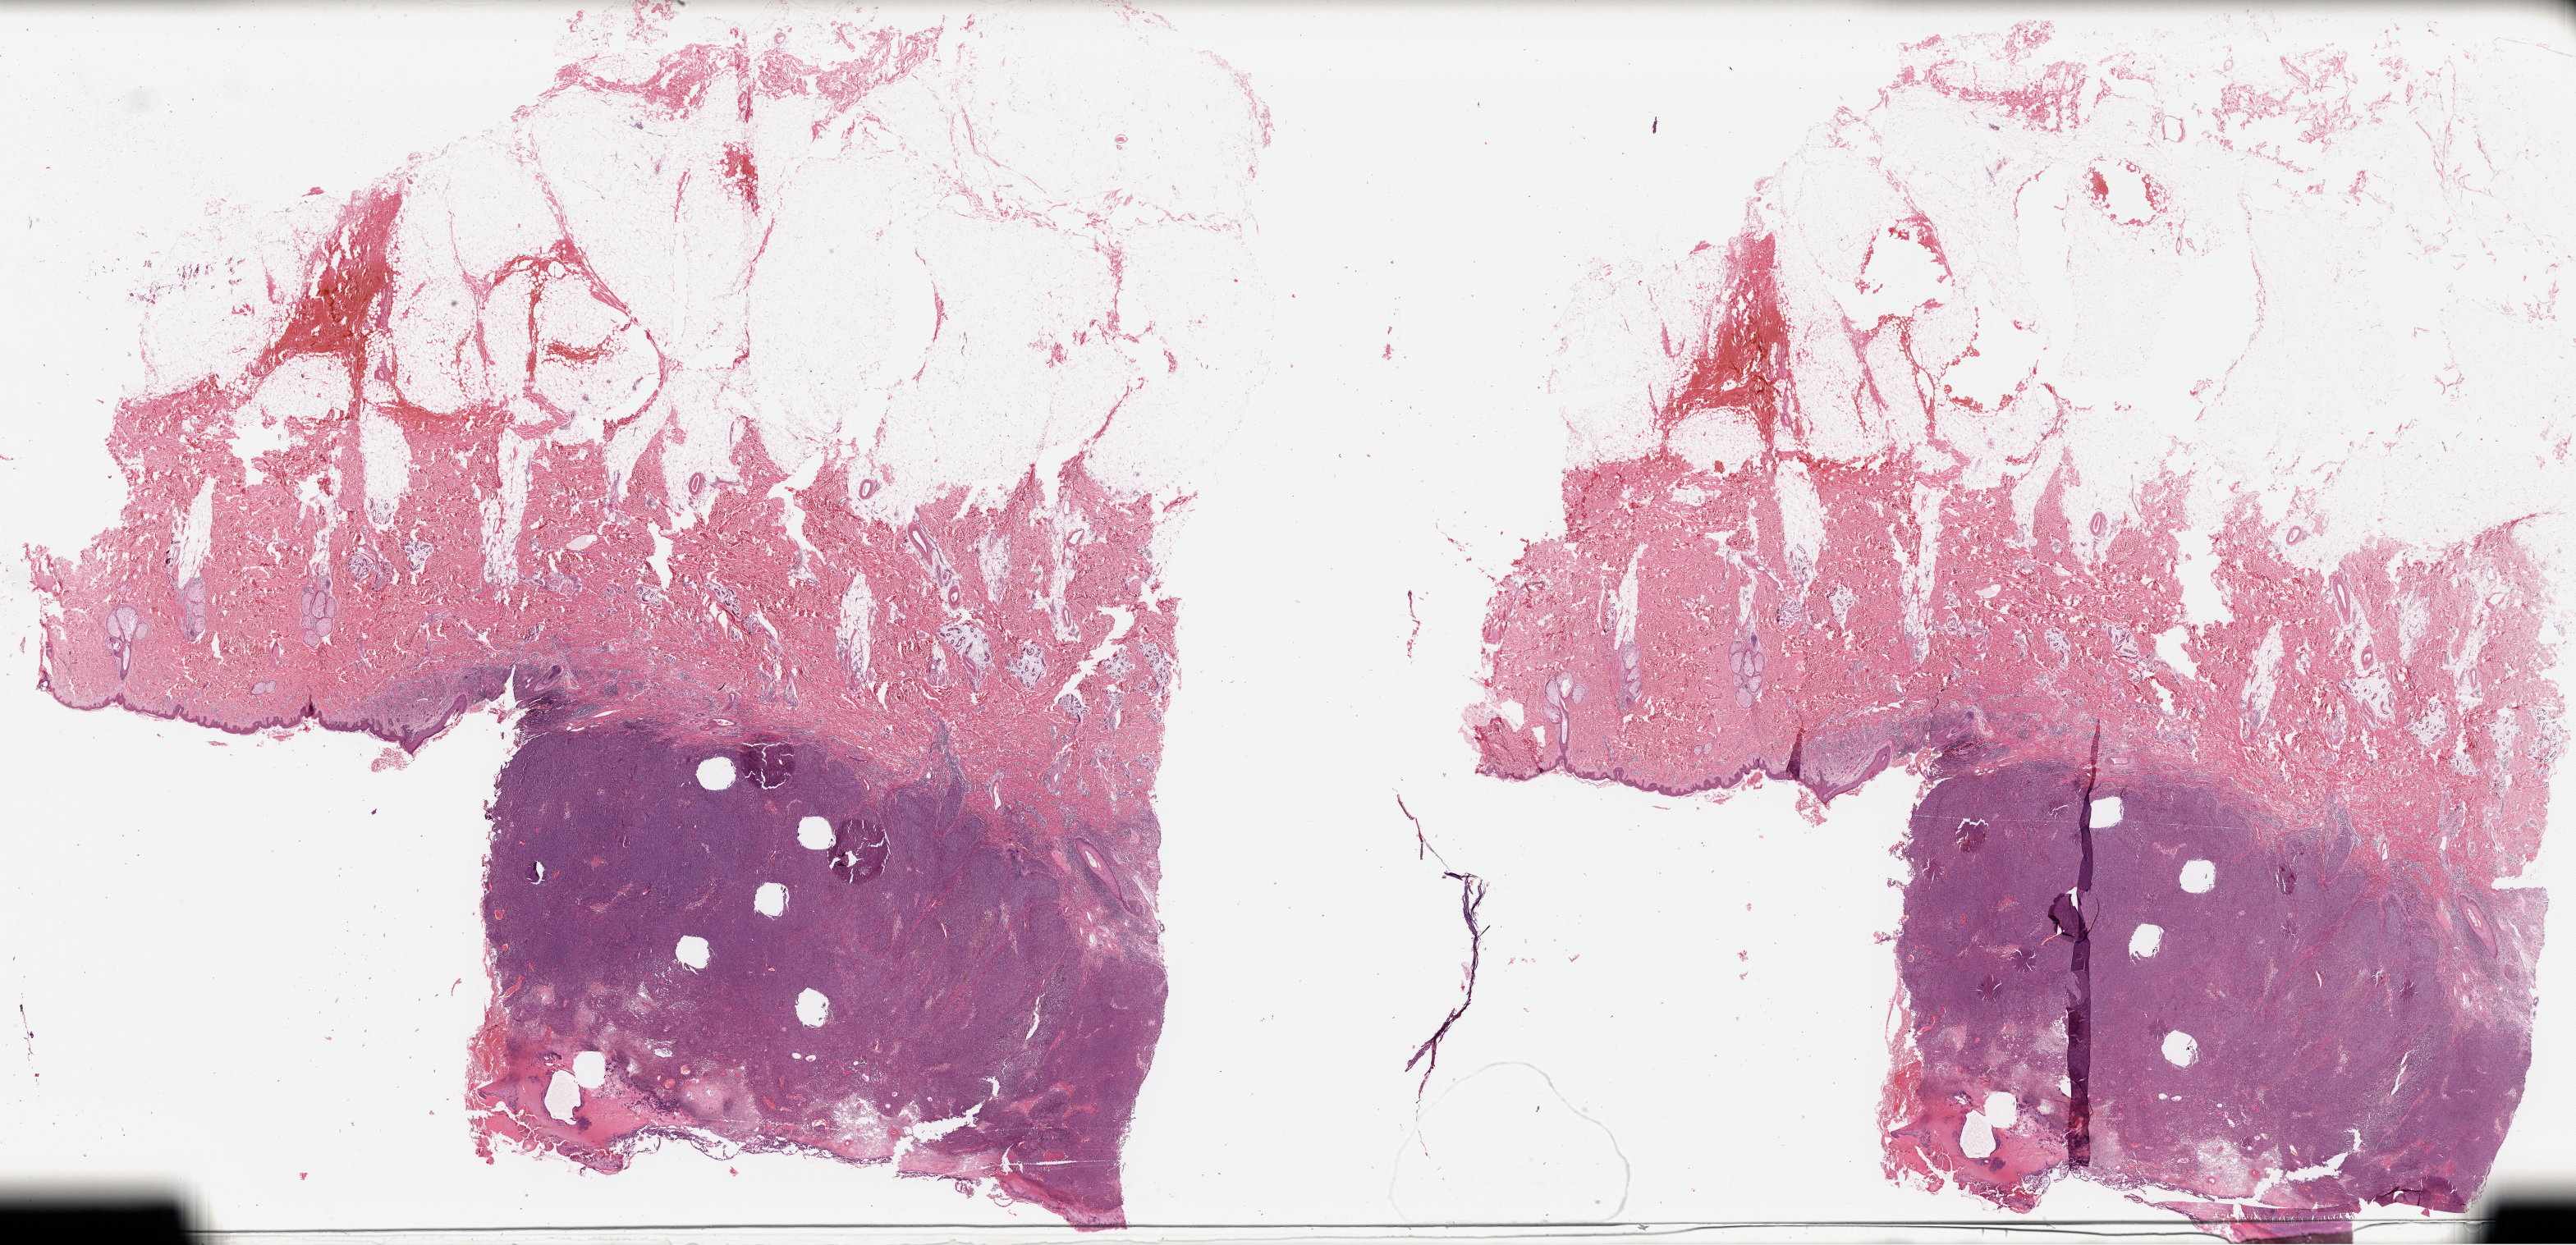
H&E-stained whole-slide image — shown as a low-resolution overview of the whole scanned area (about 49.3 x 23.8 mm, slide scanned at 40x). FFPE section. Primary tumour sample from the skin. Male, age 43 years at initial diagnosis.
• histologic diagnosis: Malignant melanoma, NOS
• AJCC pathologic stage: IIIA (5th edition)
• TNM: T4b N1a M0